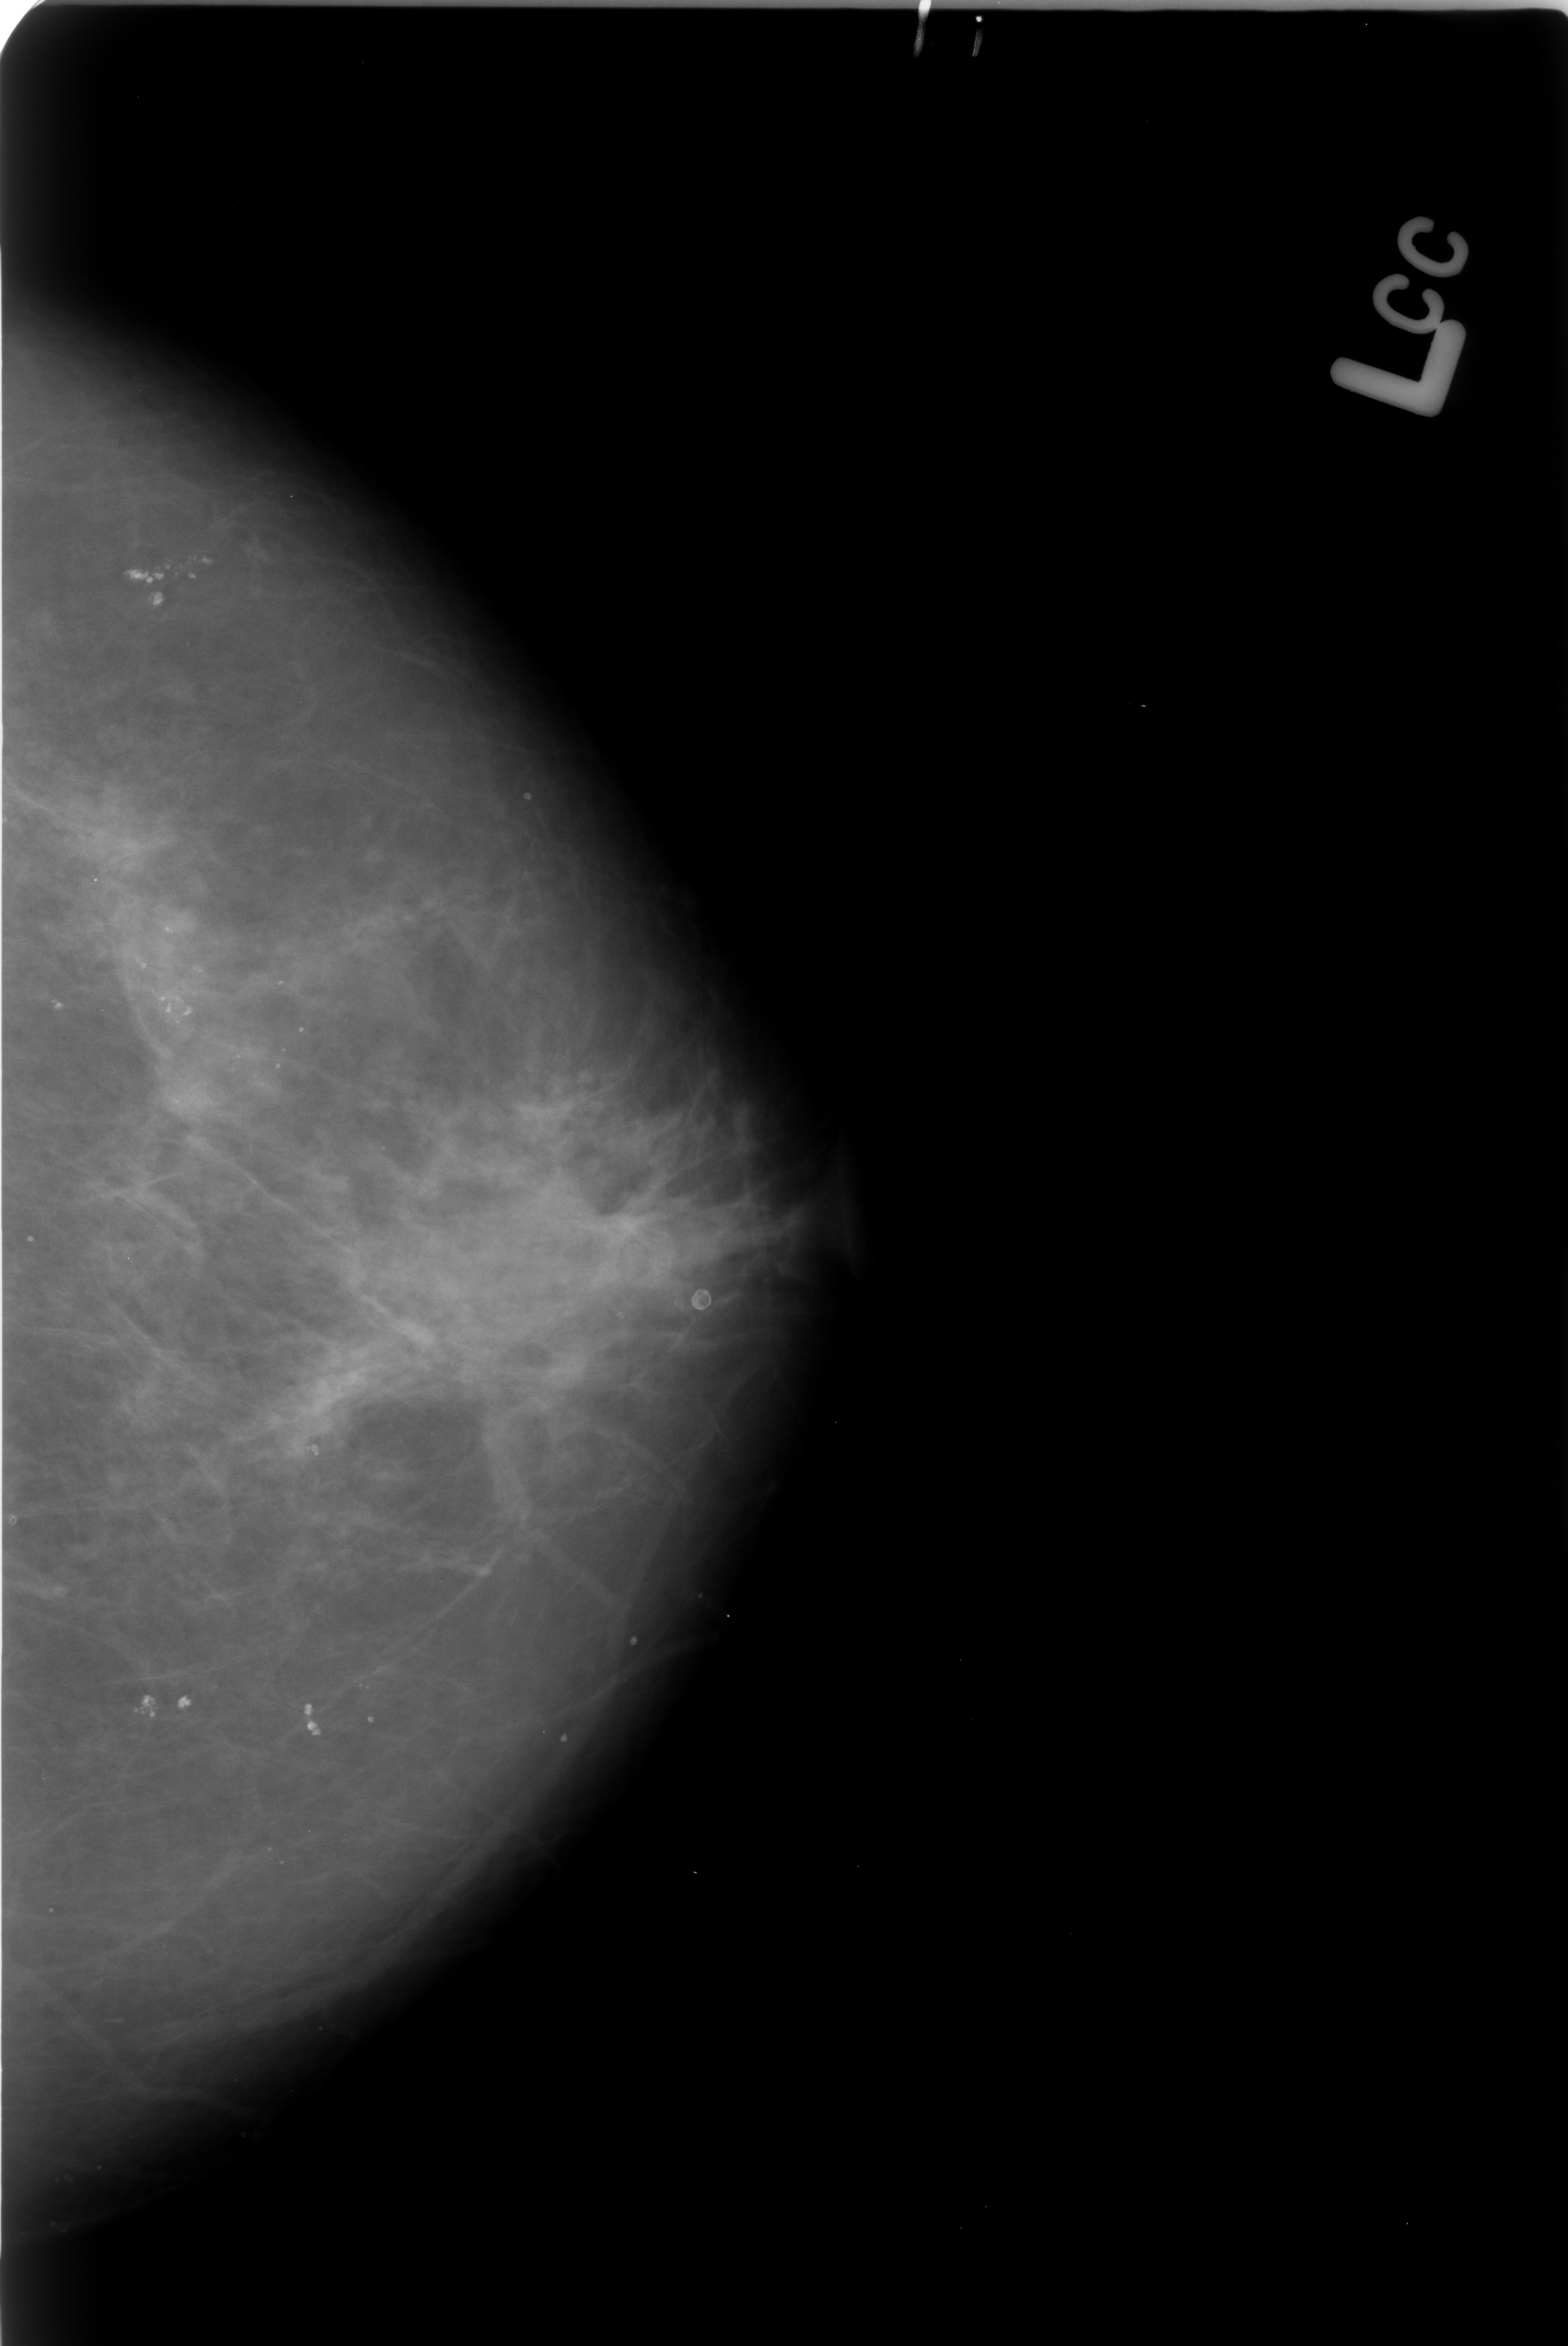
Mammogram (digitized film); left breast; CC view; BI-RADS breast density category 2 (scale 1–4).
Calcifications, morphology pleomorphic, distribution clustered; BI-RADS assessment category 4; subtlety rating 3 on a 1 (subtle) to 5 (obvious) scale; pathology result (as recorded, not read from the image): benign.